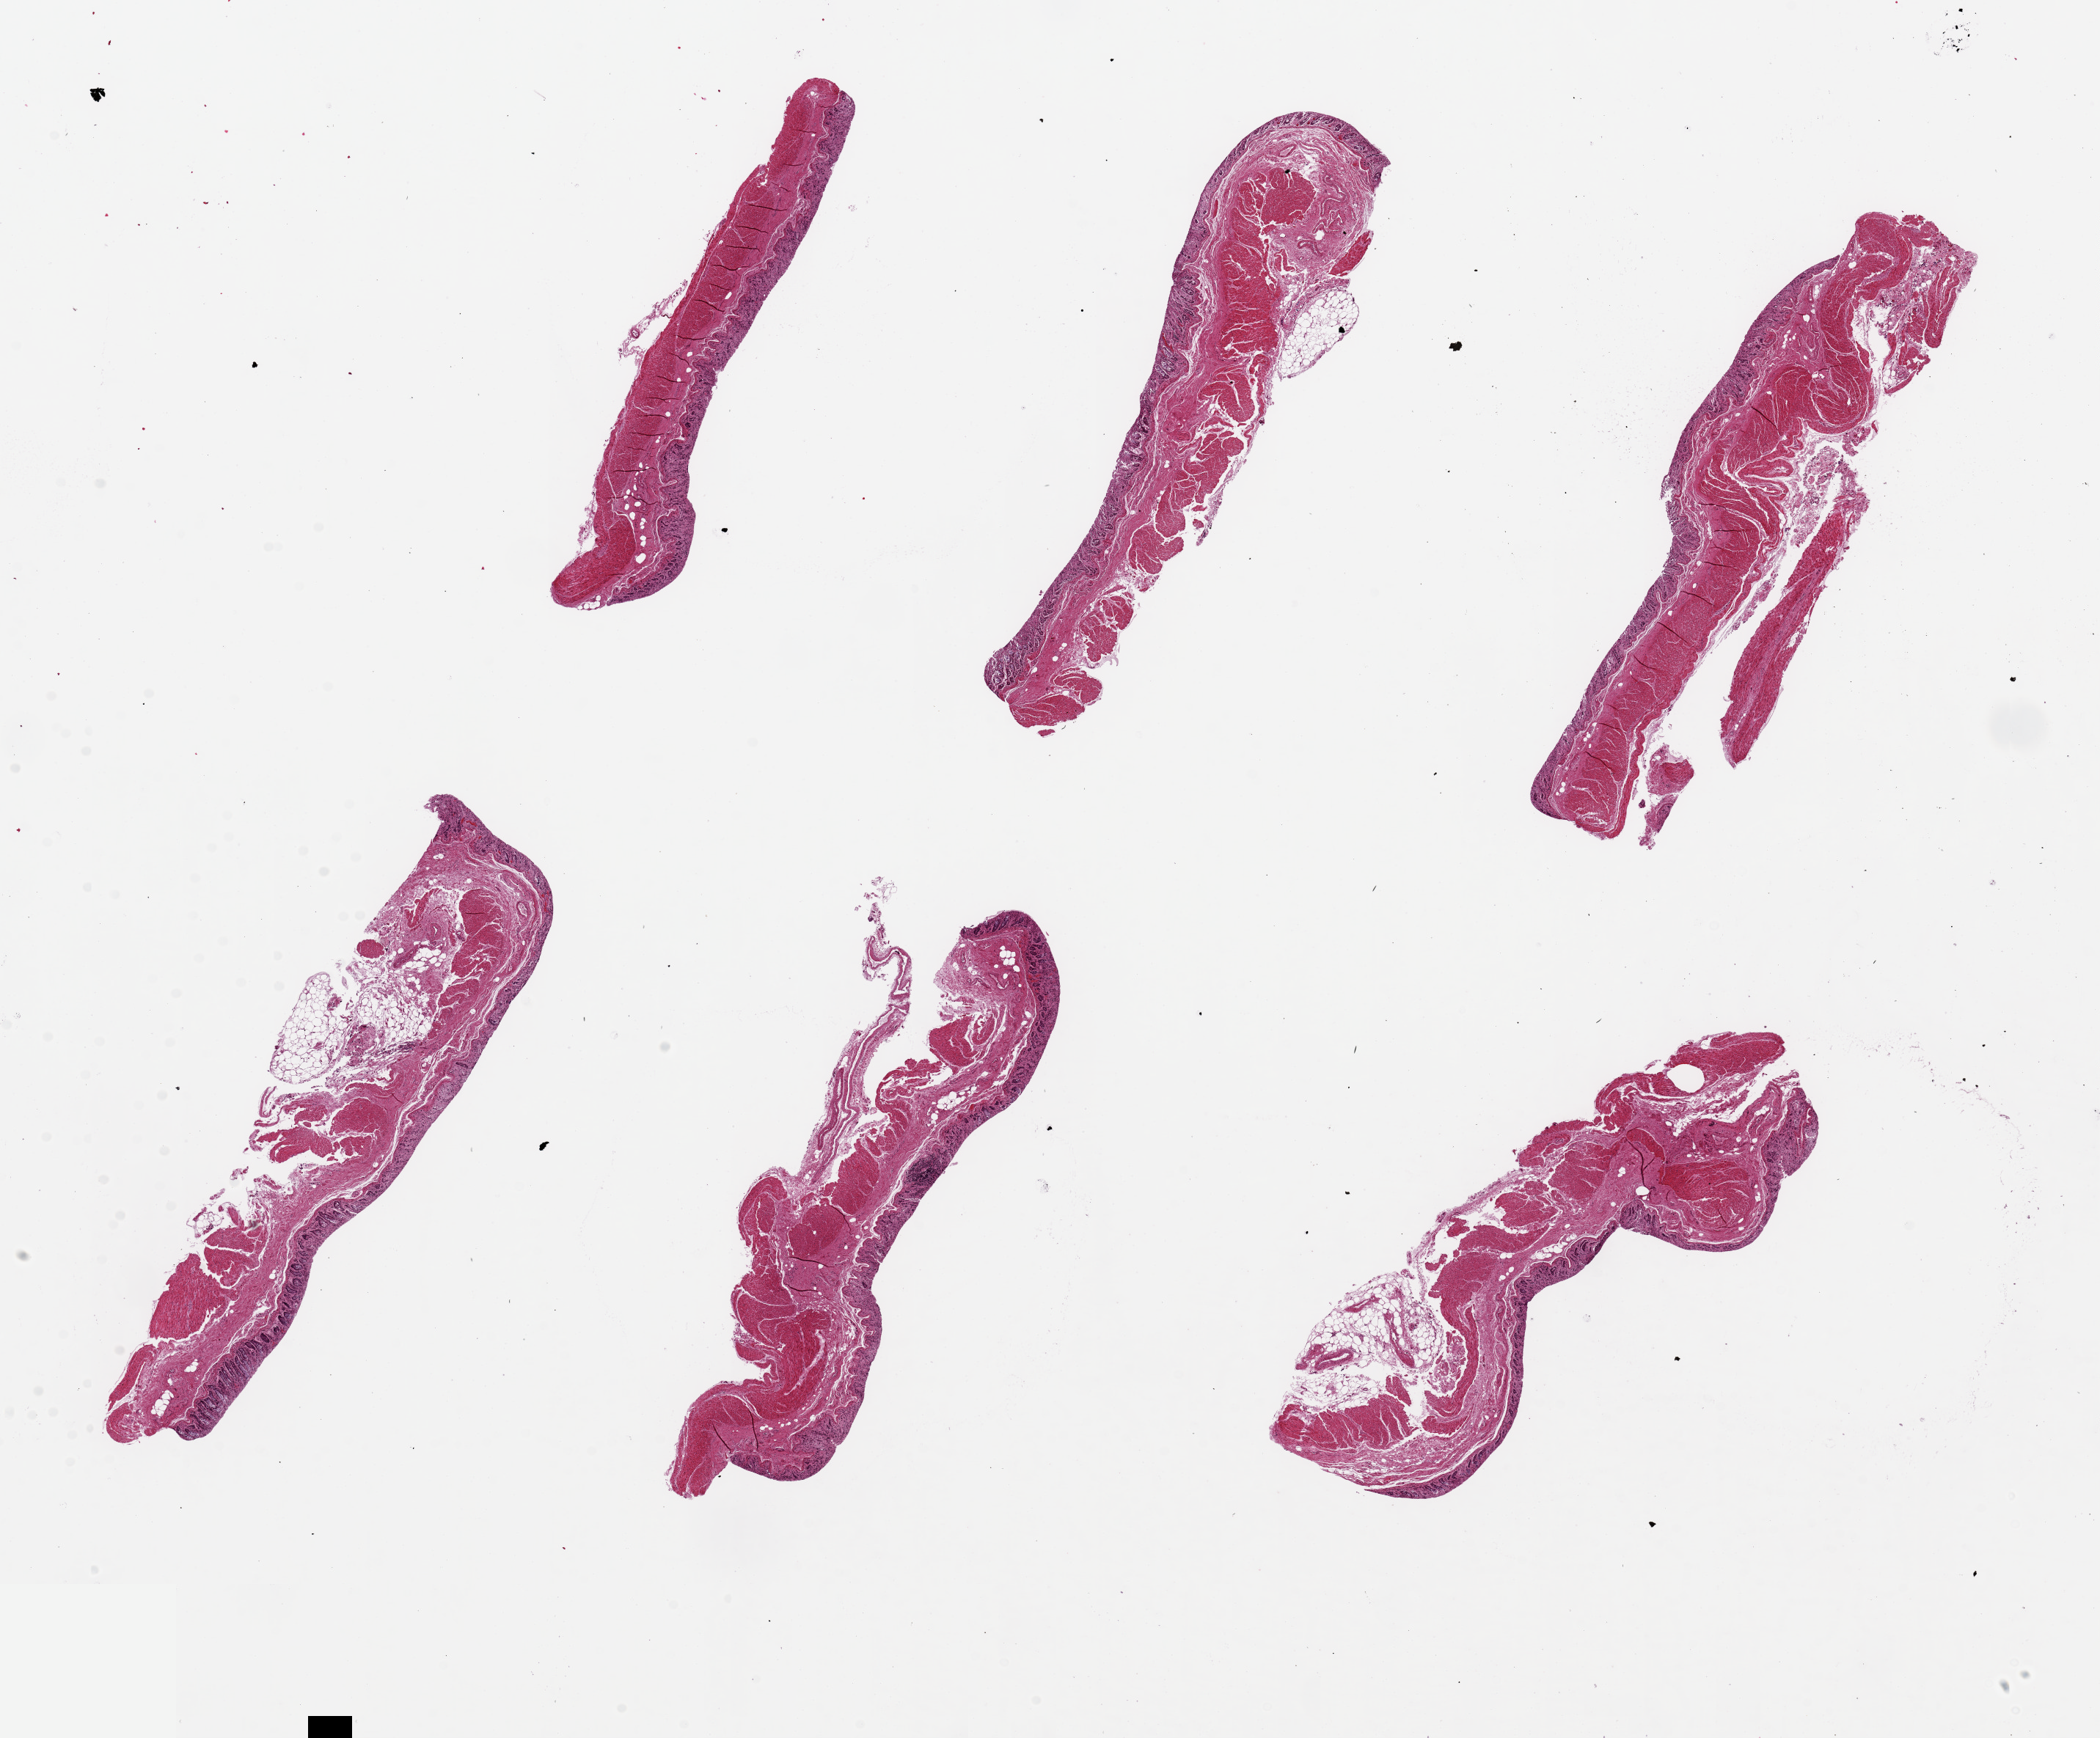
Hematoxylin and eosin (H&E) whole-slide image — a low-resolution overview of the entire scanned area, about 22.6 x 18.7 mm (slide scanned at 20x), PAXgene-fixed, paraffin-embedded tissue, section of transverse colon (target tissue), donor tissue sample. Donor: male.
Reviewer comment on this tissue sample: 6 pieces, up to 8x2mm; autolyzed mucosa (3); muscle moderately autolyzed (2).